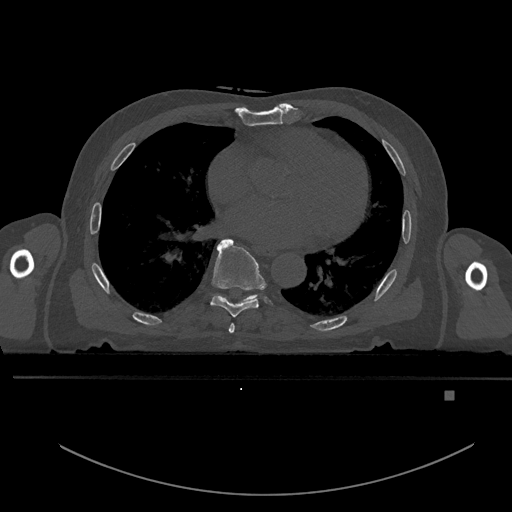
CT including the spine, one axial slice. Slice 247 of 969 in the series (ordered by position). Bone window (W 1800 / L 400 HU). 0.5 mm slice thickness. 512 × 512 image matrix, field of view 456 × 456 mm. Male patient, age 82 years. Case-level facts recorded for this patient, not image findings: primary cancer: prostate; vertebrae with lytic lesions (as recorded): T11, T9, T8, T2.
Outlined on this slice (semi-automatic segmentation, software-assisted and operator-edited):
- T6 vertebra: bounding box (x1, y1, x2, y2) in pixels: (229, 323, 235, 333)
- T7 vertebra: (210, 238, 265, 317)
- T8 vertebra: (214, 294, 258, 304)